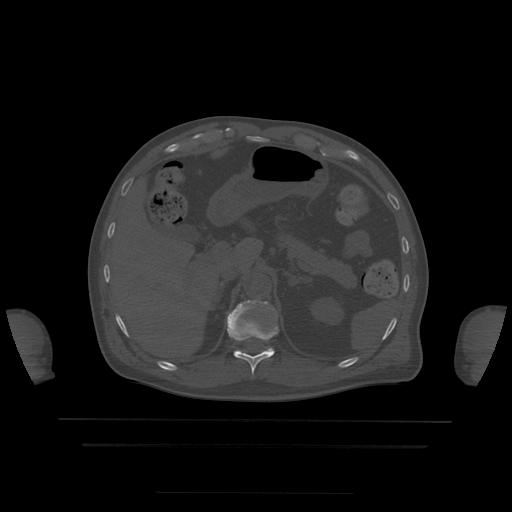
CT including the spine, one axial slice. Position 213 of 522 along the scan axis. Bone window (W 1800 / L 400 HU). 1.25 mm slice thickness. 512 × 512 image matrix, field of view 436 × 436 mm. Patient age 68 years. Case-level facts recorded for this patient, not image findings: primary cancer: urothelial.
Outlined on this slice (semi-automatically segmented with operator editing):
- T11 vertebra: bounding box [x1, y1, x2, y2] px = [227, 301, 279, 374]
- T12 vertebra: [240, 348, 273, 353]